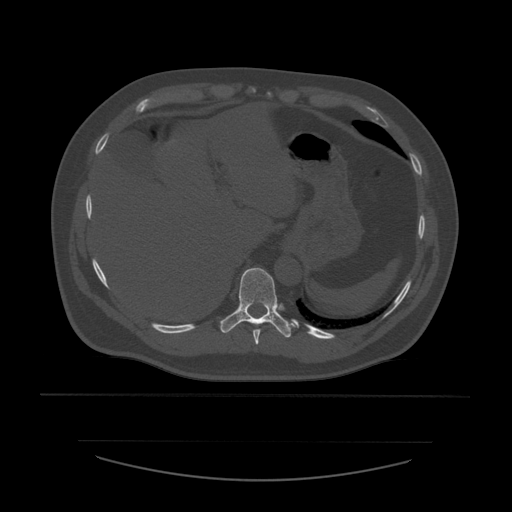
CT including the spine, one axial slice; position 301 of 532 along the scan axis; bone window (W 1800 / L 400 HU); 512 × 512 image matrix, field of view 441 × 441 mm. Patient age 44 years. Case-level facts recorded for this patient, not image findings: primary cancer: soft tissue sarcoma.
Annotated regions visible in this slice (semi-automatic segmentation, software-assisted and operator-edited):
- T10 vertebra: box from (x=220, y=268) to (x=298, y=338) px
- T9 vertebra: (x=253, y=324)–(x=261, y=345)